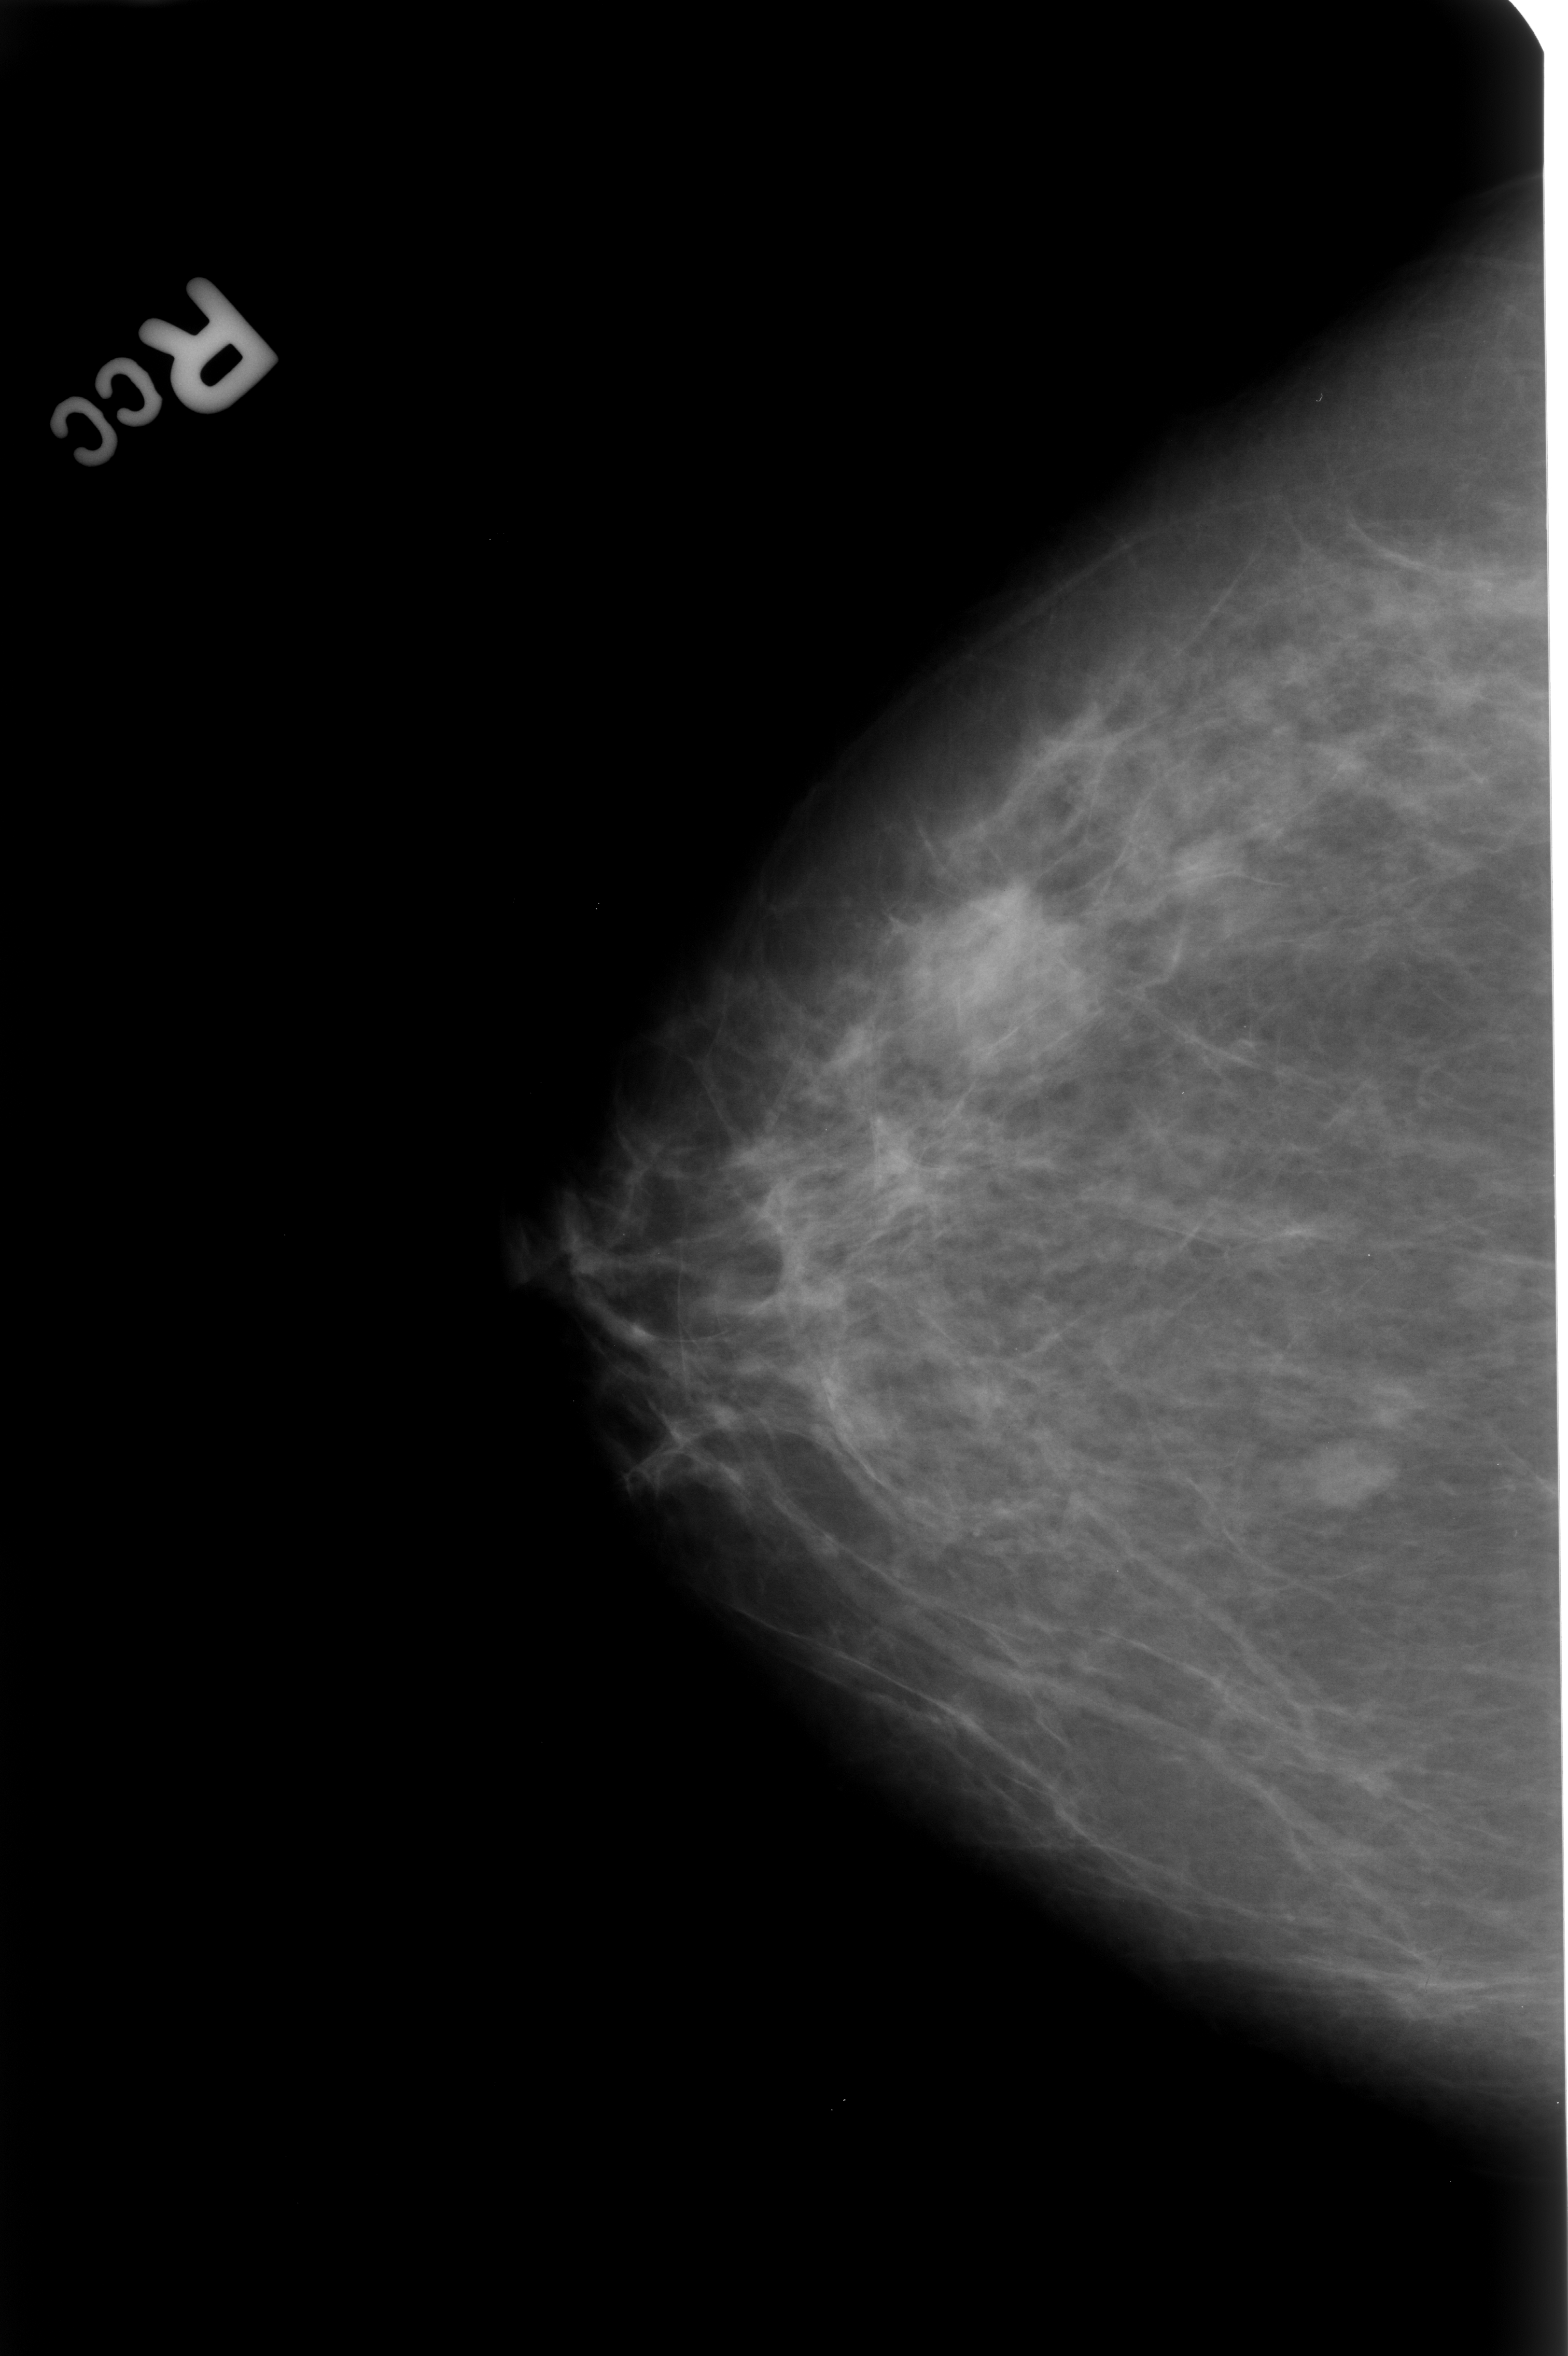
Digitized screen-film mammogram, right breast, craniocaudal (CC) view, BI-RADS breast density category 2 (scale 1–4).
- Abnormality record for this image: mass, shape lobulated, margins circumscribed / ill defined; BI-RADS assessment category 4; subtlety rating 4 on a 1 (subtle) to 5 (obvious) scale; pathology (as recorded): benign.